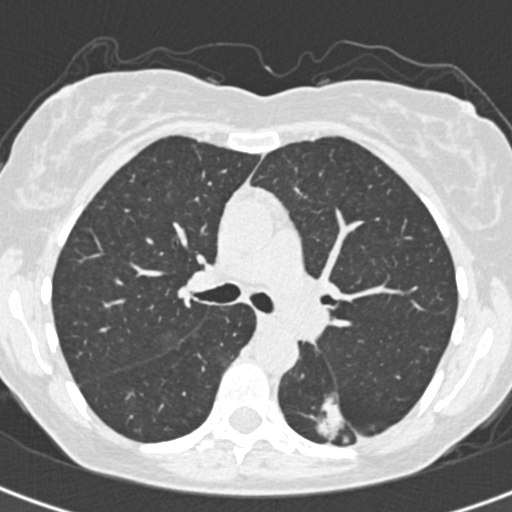
Low-dose screening chest CT, one axial slice; slice 210 of 328 in the series (ordered by position); reconstruction kernel B30f; 120 kVp; lung window (W 1500 / L -600 HU); 1 mm slice thickness; 512 × 512 image matrix, field of view 284 × 284 mm.
Structures marked on this image (outlined manually by an expert reader):
- lesion 1 (tumor, lower lobe of left lung): bounding box [x1, y1, x2, y2] px = [317, 397, 347, 441]